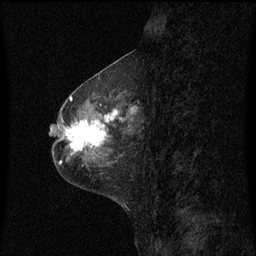
Breast MRI (dynamic contrast-enhanced), one sagittal slice. Slice 24 of 60 in the series (ordered by position). Dynamic contrast-enhanced series, image 2 of 3 at this slice position (ordered by acquisition). 1.5 T. TE 4.2 ms, TR 8.4 ms. 2 mm slice thickness. 256 × 256 image matrix, field of view 200 × 200 mm. Patient: female, 49 years. From the clinical record (not read from this slice): setting: breast cancer imaged before/during neoadjuvant chemotherapy; receptor status: HR-positive, HER2-negative.
Structures marked on this image (semi-automatically segmented with operator editing):
- analysis volume of interest (the breast-tissue region the enhancement analysis was run in; not a lesion): bounding box [x1, y1, x2, y2] px = [59, 101, 137, 158]
- tumour enhancement mask (voxels above the 70 % enhancement threshold inside the analysis volume of interest): [67, 109, 134, 152]